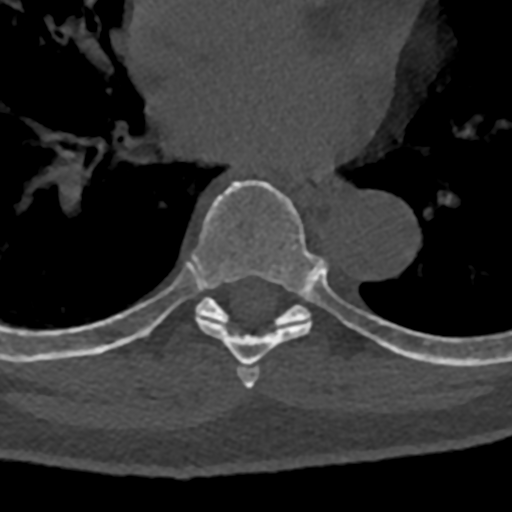
CT including the spine, one axial slice. Position 746 of 797 along the scan axis. Reconstruction kernel Br40s/3. 120 kVp. Bone window (W 1800 / L 400 HU). 0.5 mm slice thickness. 512 × 512 image matrix, field of view 160 × 160 mm. Patient: male, 74 years. From the clinical record (not read from this slice): primary cancer: renal; vertebrae with lytic lesions (as recorded): T10, L1, L2, L3, L4, L5.
Outlined on this slice (semi-automatic segmentation, software-assisted and operator-edited):
- T6 vertebra: bounding box (x1, y1, x2, y2) in pixels: (237, 366, 259, 389)
- T7 vertebra: (71, 180, 392, 367)
- T8 vertebra: (70, 296, 432, 363)